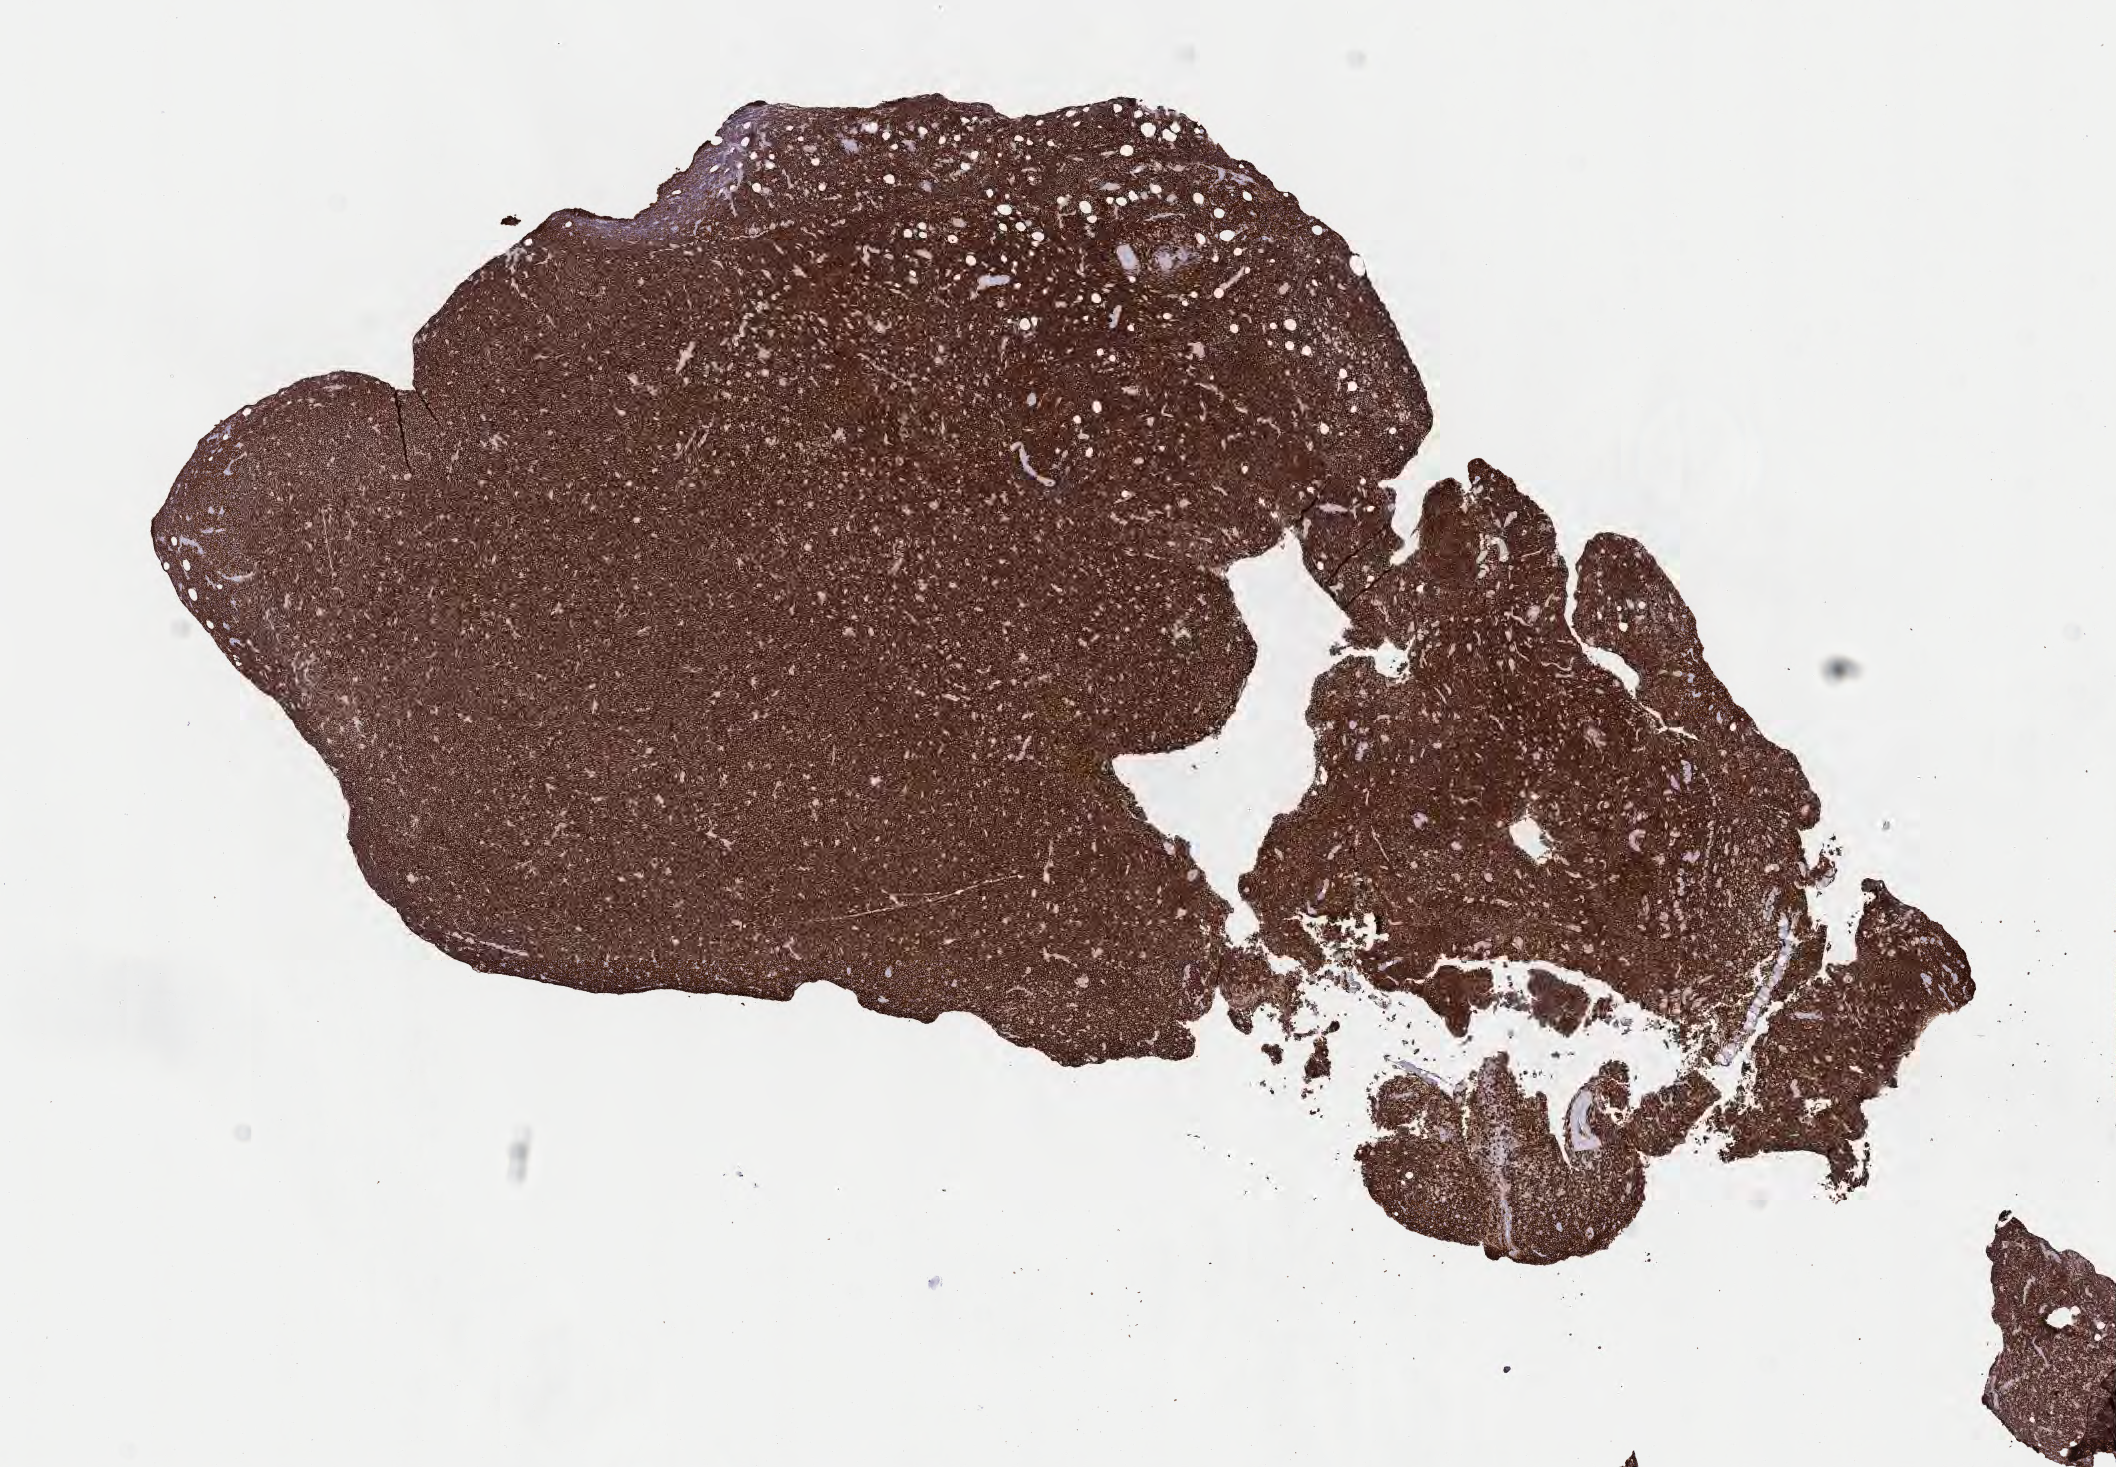
Whole-slide image, immunohistochemical stain for CD20, low-resolution overview of the scanned area, about 8.6 x 5.9 mm. Tumor tissue. Patient female; aged 40.
- diagnosis: Burkitt lymphoma, NOS